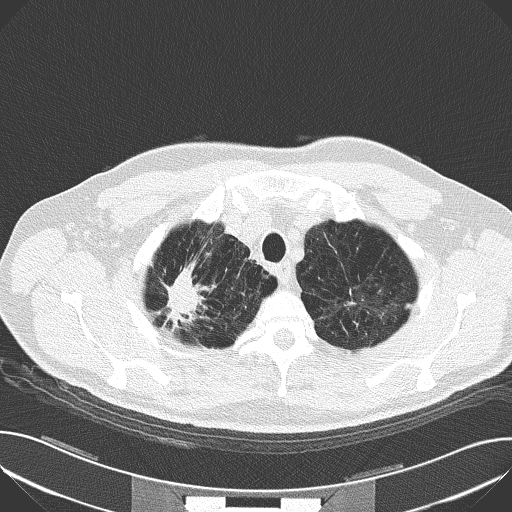
Chest CT (low-dose screening protocol), one axial image; first (baseline) screen; lung window (W 1500 / L -600 HU); lung (sharp) reconstruction kernel (B50f); slice 20 of 159 in the series; 512 × 512 image matrix, field of view 380 × 380 mm. Male participant, aged 59 years at enrolment. Current smoker at enrolment.
• Expert reader's lesion annotation, bounding box [x1, y1, x2, y2] px = [155, 260, 221, 331].
• The screening reader recorded 4 non-calcified nodules or masses ≥4 mm on this exam (right upper lobe, left upper lobe, right upper lobe, left upper lobe); which of them this box marks is not recorded.
• Official screen result: positive, change unspecified: nodule(s) >= 4 mm or enlarging nodule(s), mass(es), or other non-specific abnormalities suspicious for lung cancer.
• Participant outcome: lung cancer diagnosed 44 days after this screen — squamous cell carcinoma, NOS, right upper lobe, moderately differentiated (G2), stage IA (AJCC 6th edition), 30 mm at pathology.